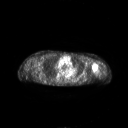
FDG PET of an extremity soft-tissue mass (from a PET/CT study), one axial slice. Slice 185 of 267 in the series (ordered by position). 128 × 128 image matrix. Female patient, age 83 years. Case-level facts recorded for this patient, not image findings: histological type: pleiomorphic leiomyosarcoma; grade: high; site of the primary tumour: left biceps.
Structures marked on this image (expert contour drawn on MRI and transferred to this co-registered scan by the dataset authors):
- gross tumour volume including surrounding oedema: box from (x=91, y=63) to (x=97, y=73) px
- gross tumour volume (mass): (x=92, y=64)–(x=97, y=70)